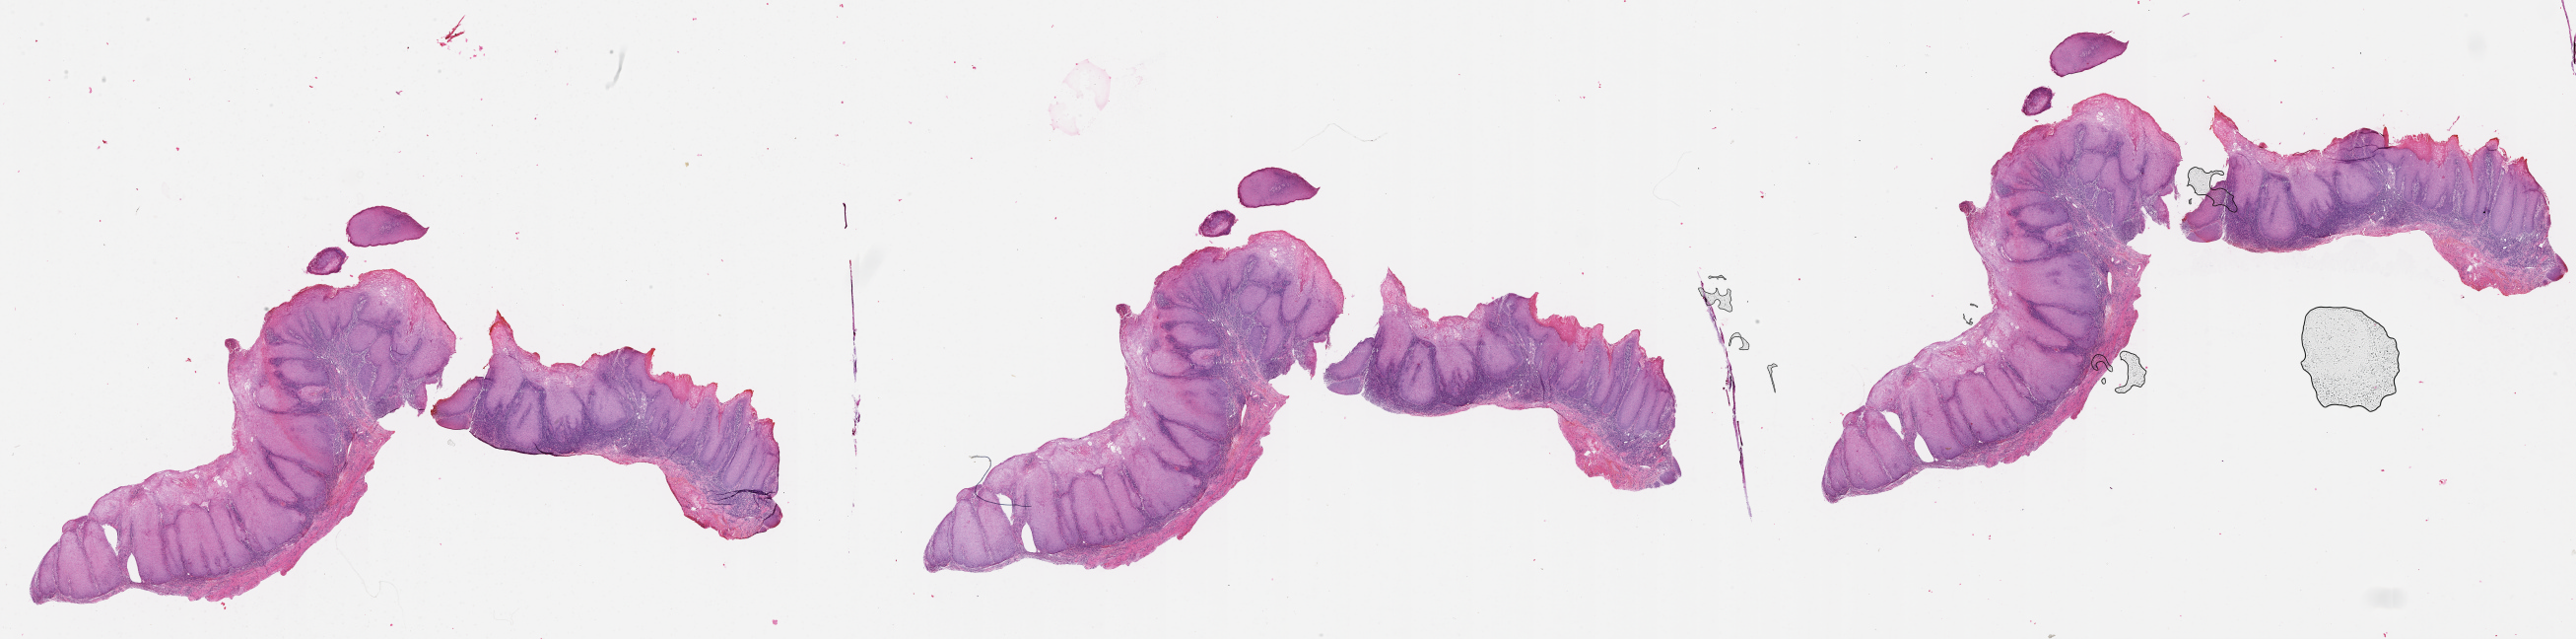
Whole-slide histology image, Hematoxylin and eosin (H&E) stained — a low-resolution overview of the entire scanned area, about 42.1 x 10.4 mm, head and neck, tissue type not recorded. Patient: male, age 69 years.
Patient diagnosis: Squamous cell carcinoma, NOS (cheek mucosa).